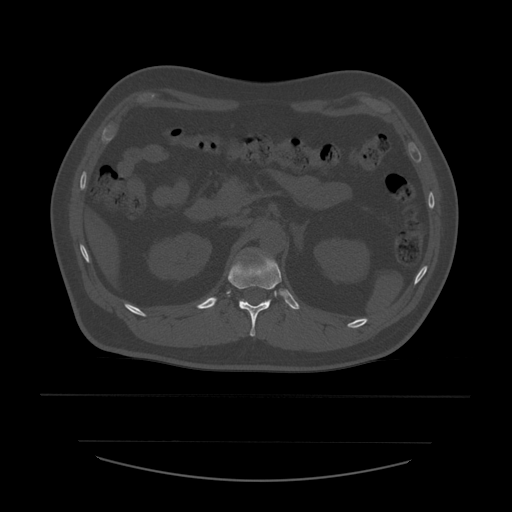
CT including the spine, one axial slice; position 246 of 532 along the scan axis; reconstruction kernel STANDARD; 120 kVp; bone window (W 1800 / L 400 HU); 1.25 mm slice thickness; 512 × 512 image matrix, field of view 441 × 441 mm. Patient age 44 years. Case-level facts recorded for this patient, not image findings: primary cancer: soft tissue sarcoma.
Outlined on this slice (semi-automatic segmentation, software-assisted and operator-edited):
- T12 vertebra: bounding box <228,252,282,337> (left, top, right, bottom; pixels)